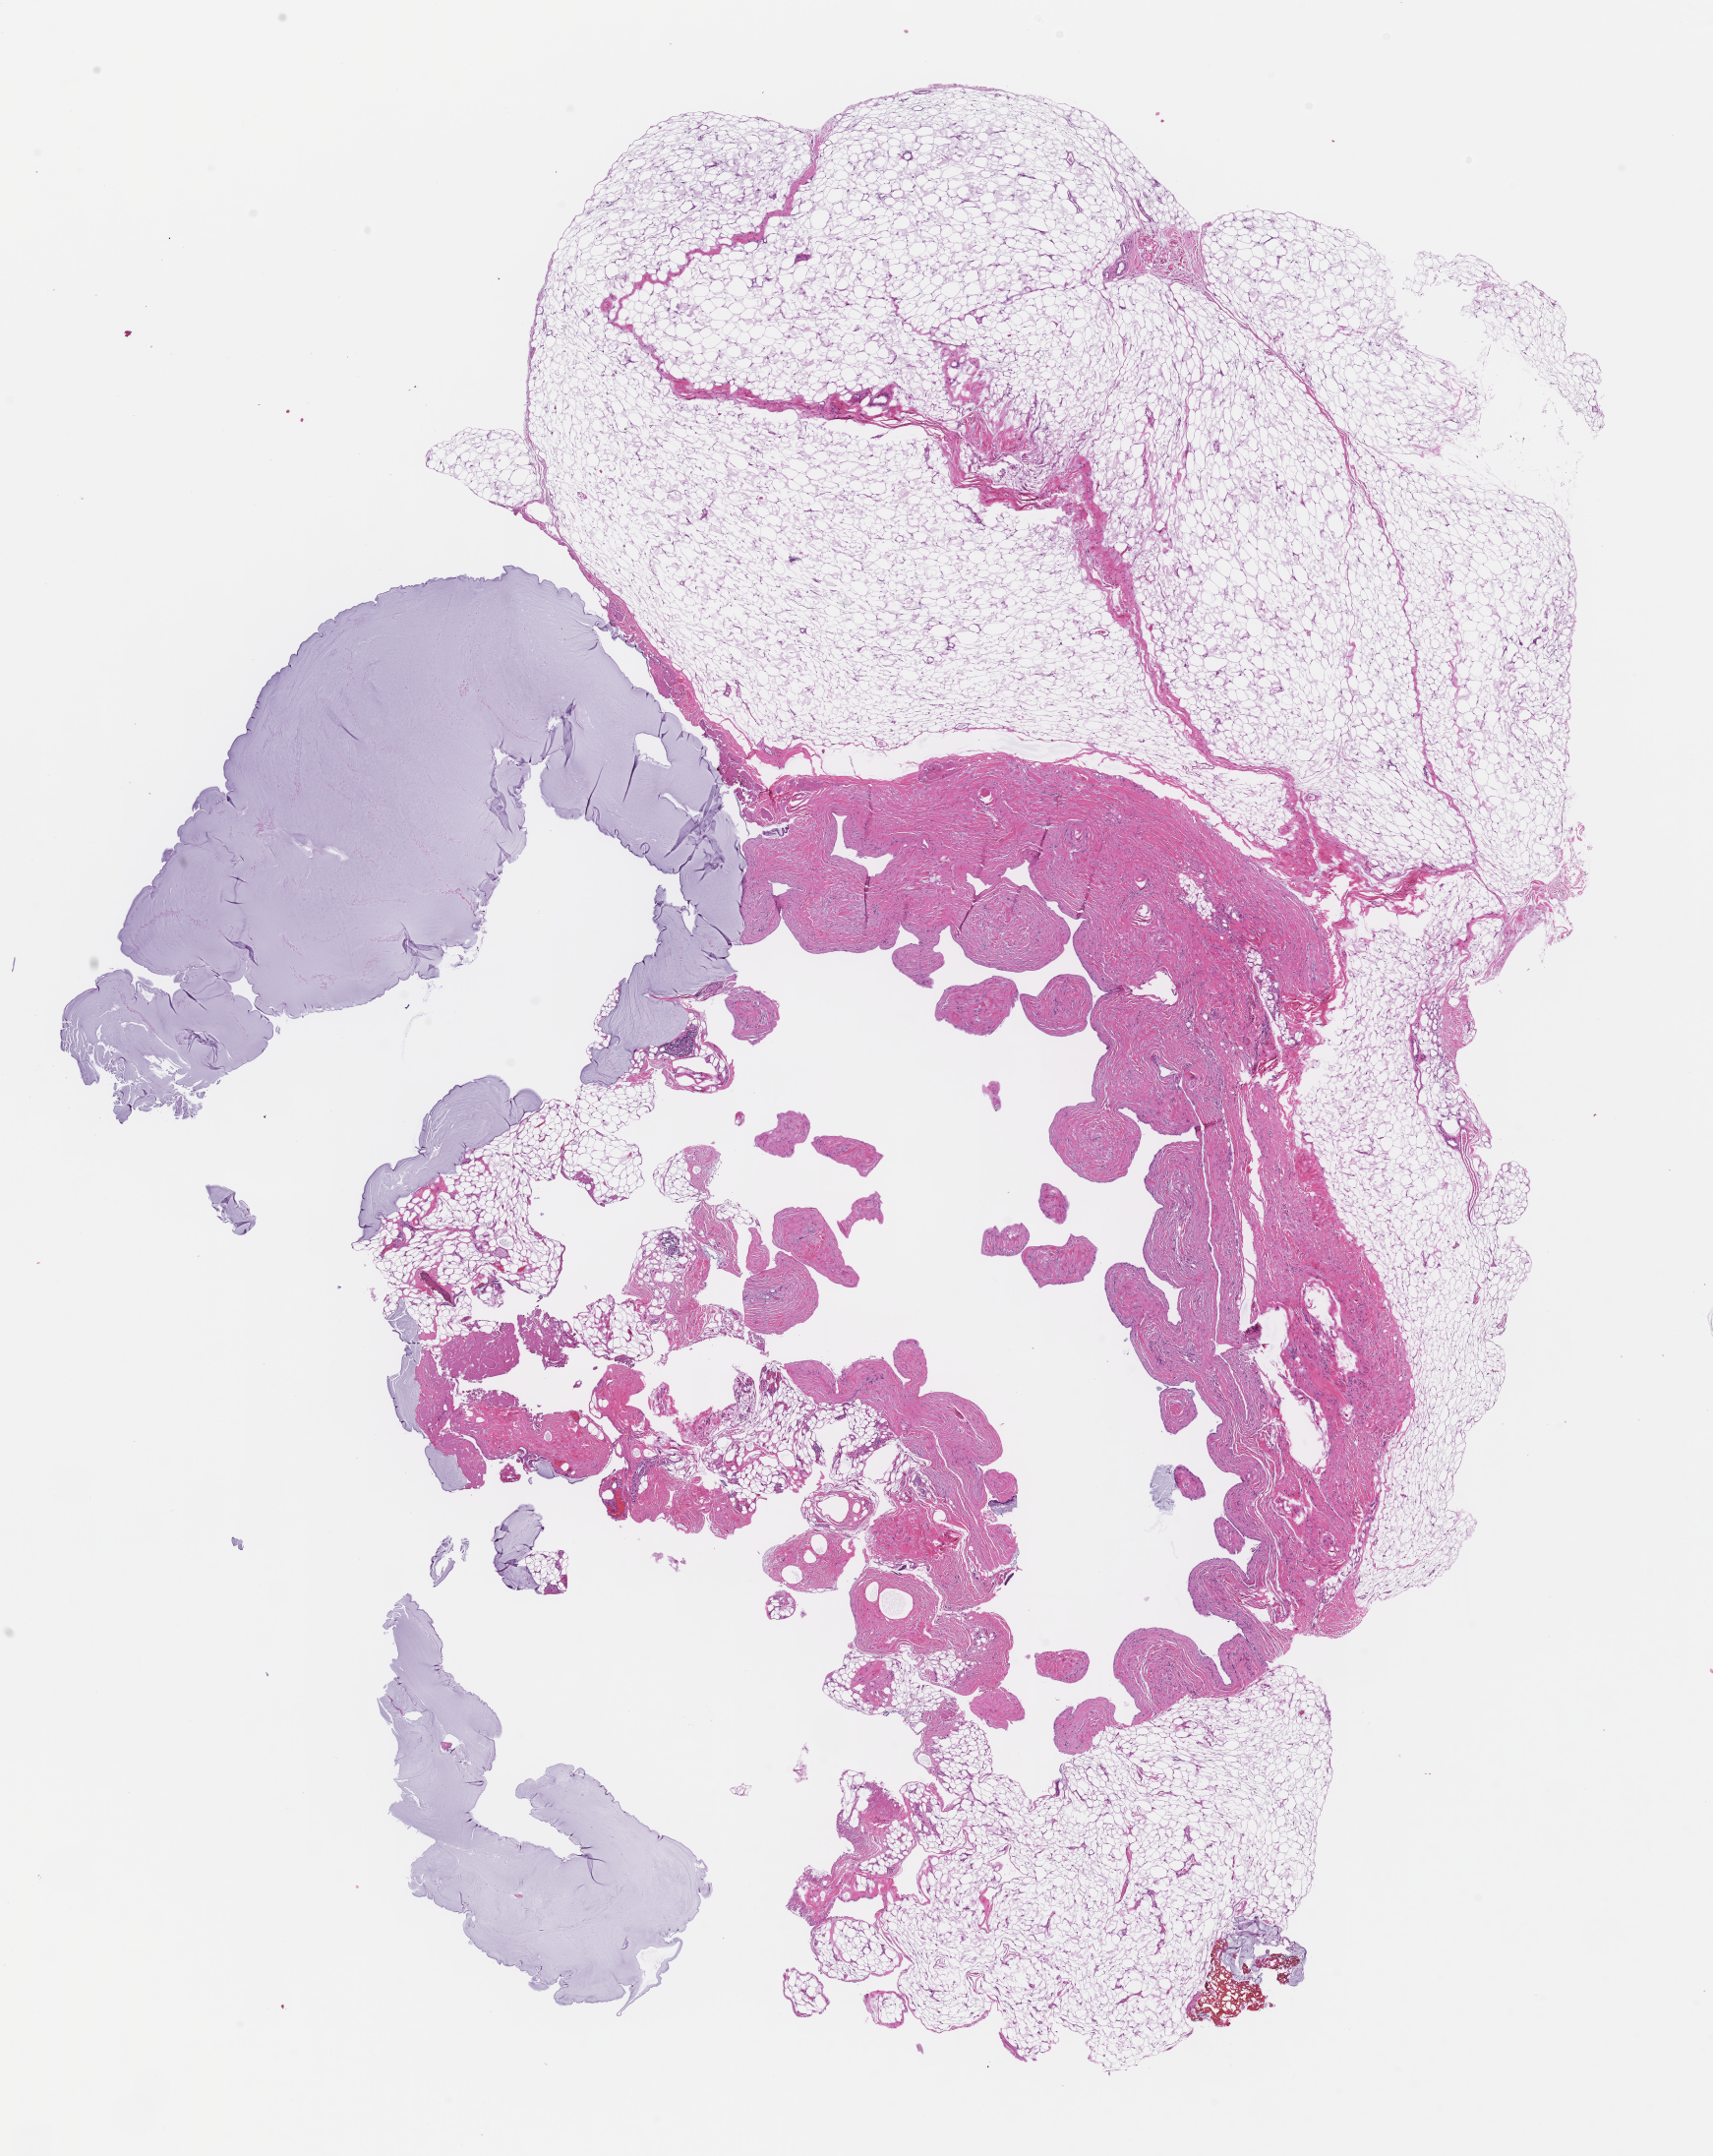
Whole-slide image, H&E stain, low-resolution overview of the scanned area, about 14.1 x 17.7 mm, formalin-fixed paraffin-embedded section. Patient sex: male.
- this section: metastasis (sampled organ not recorded)
- patient diagnosis (primary): Colorectal Carcinoma